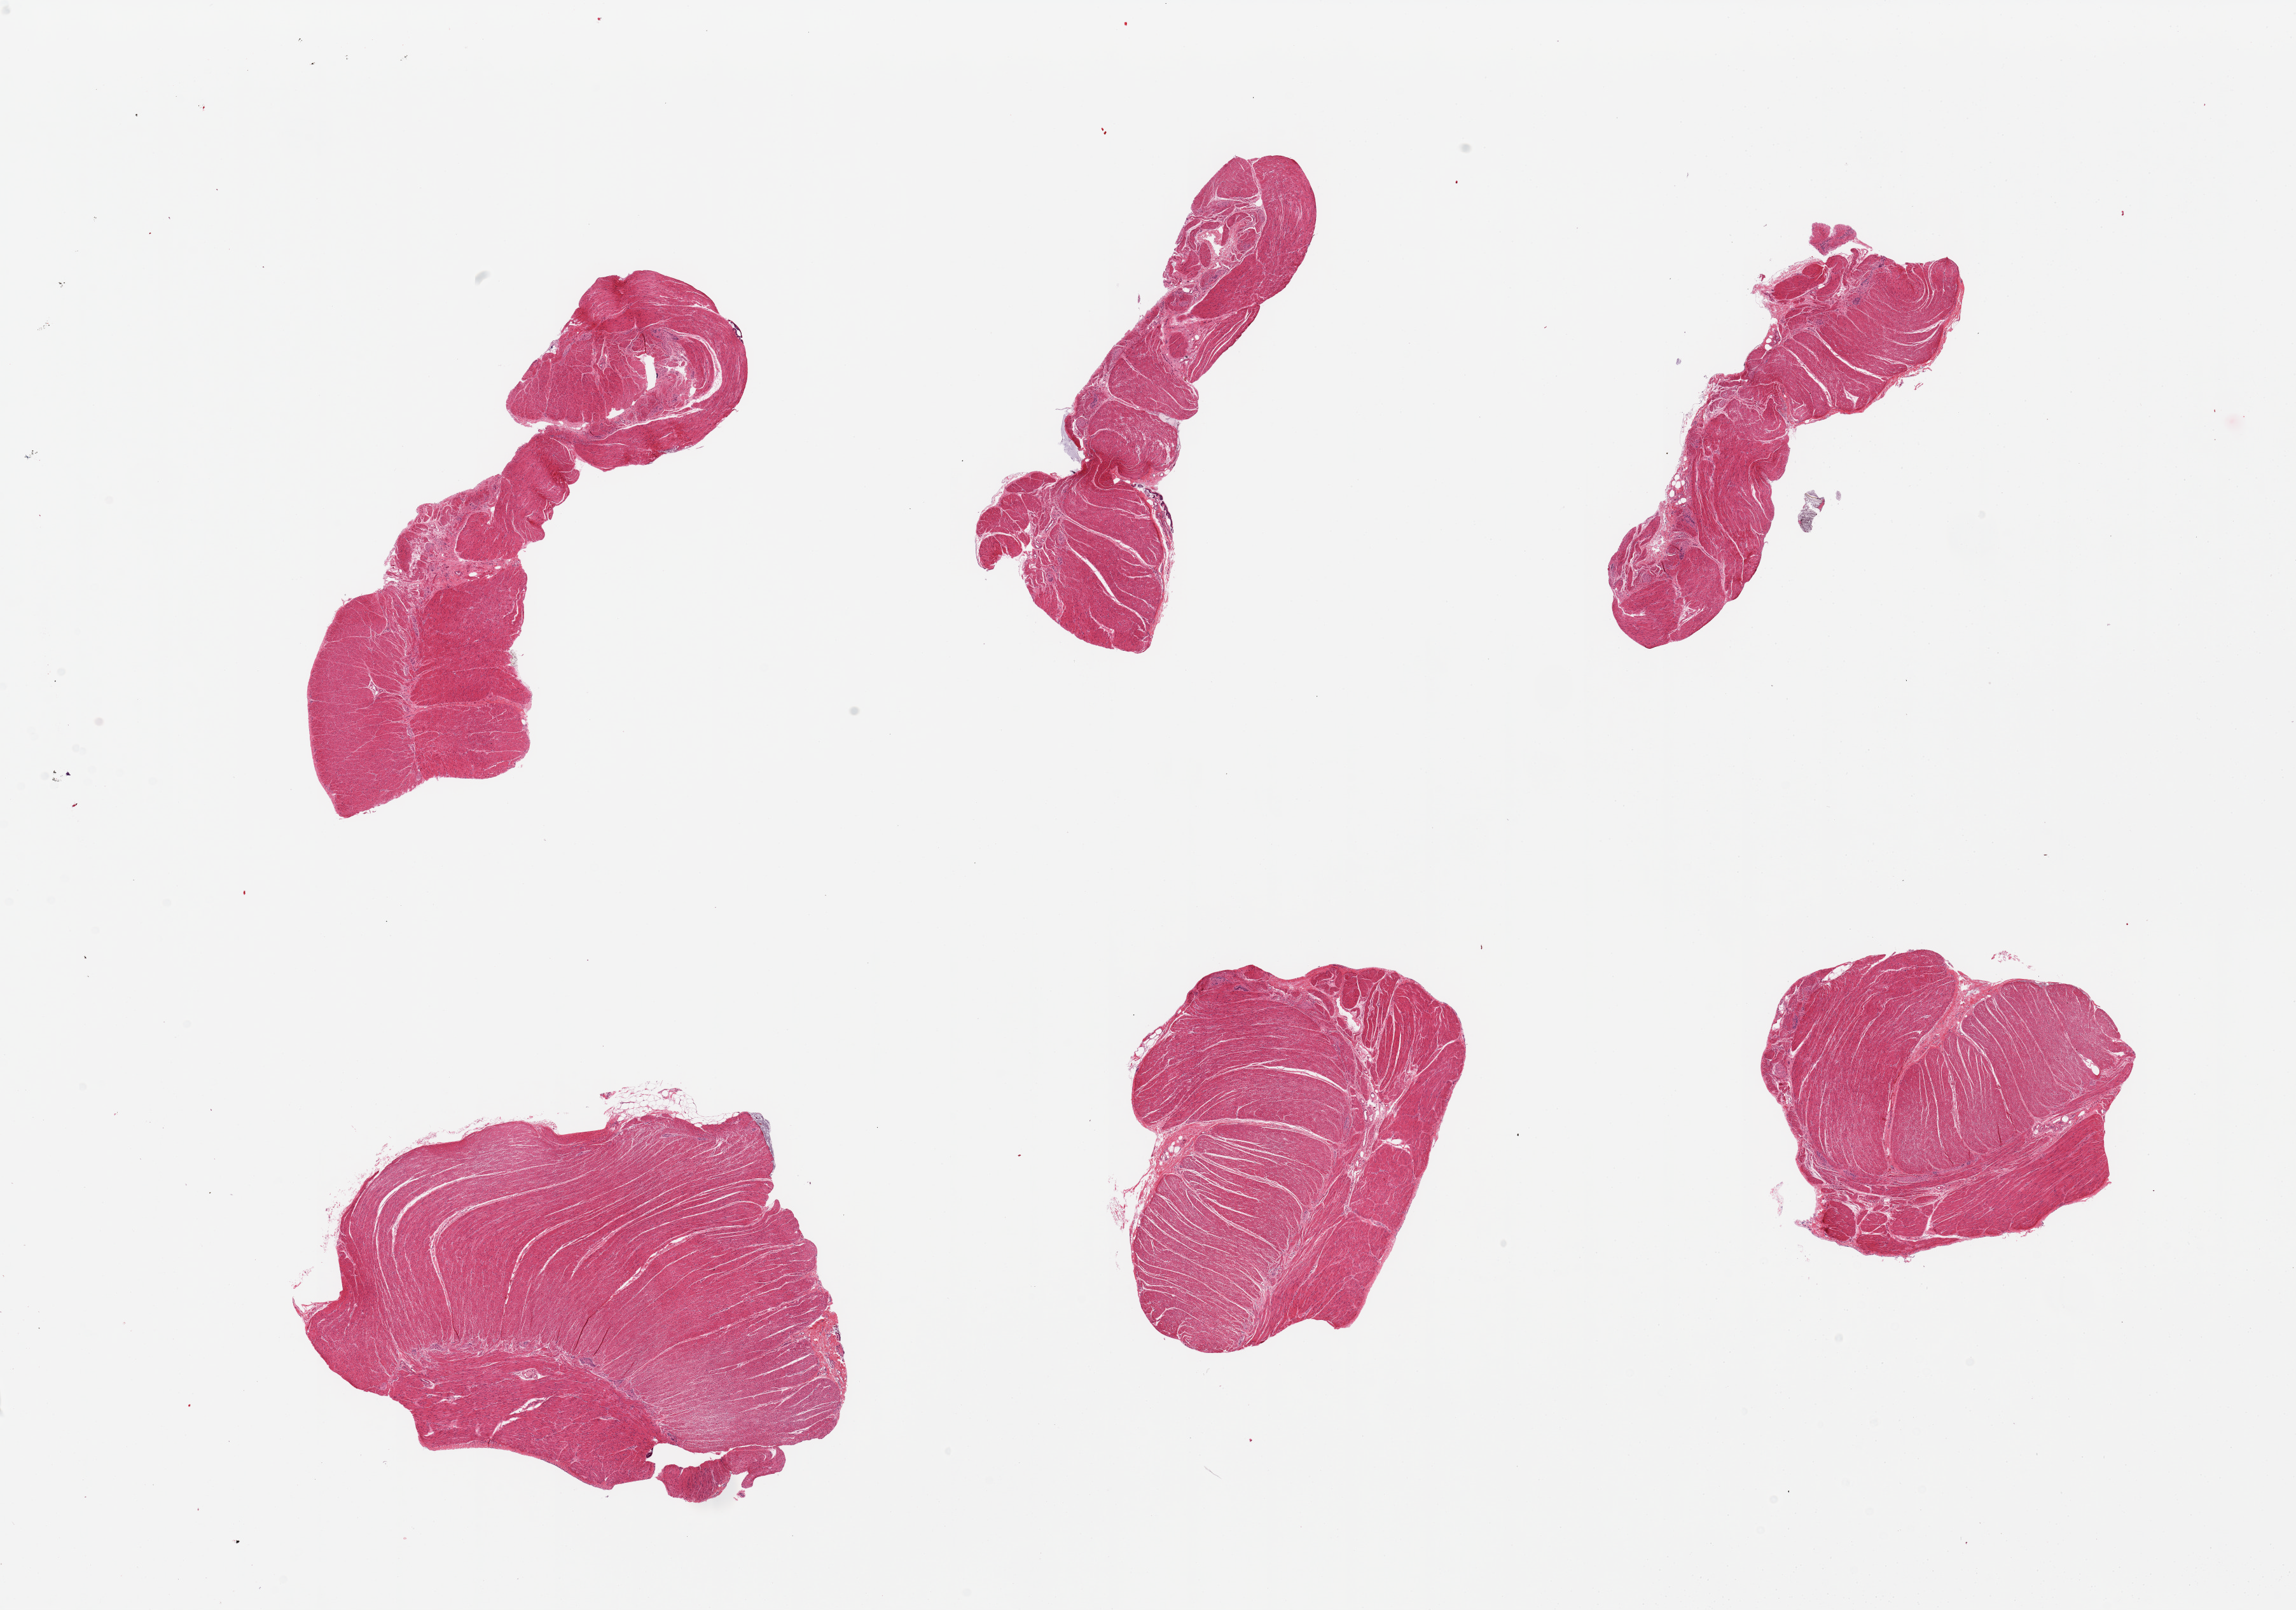
Digitized hematoxylin and eosin (H&E)-stained section, whole scanned area (about 28.5 x 20.0 mm) shown as a low-resolution overview. PAXgene-fixed paraffin-embedded (PFPE) section. Section of sigmoid colon (target tissue). Tissue donor sample. Donor: male.
- pathologist's review note for this sample: 6 pieces: all well dissected muscularis propria